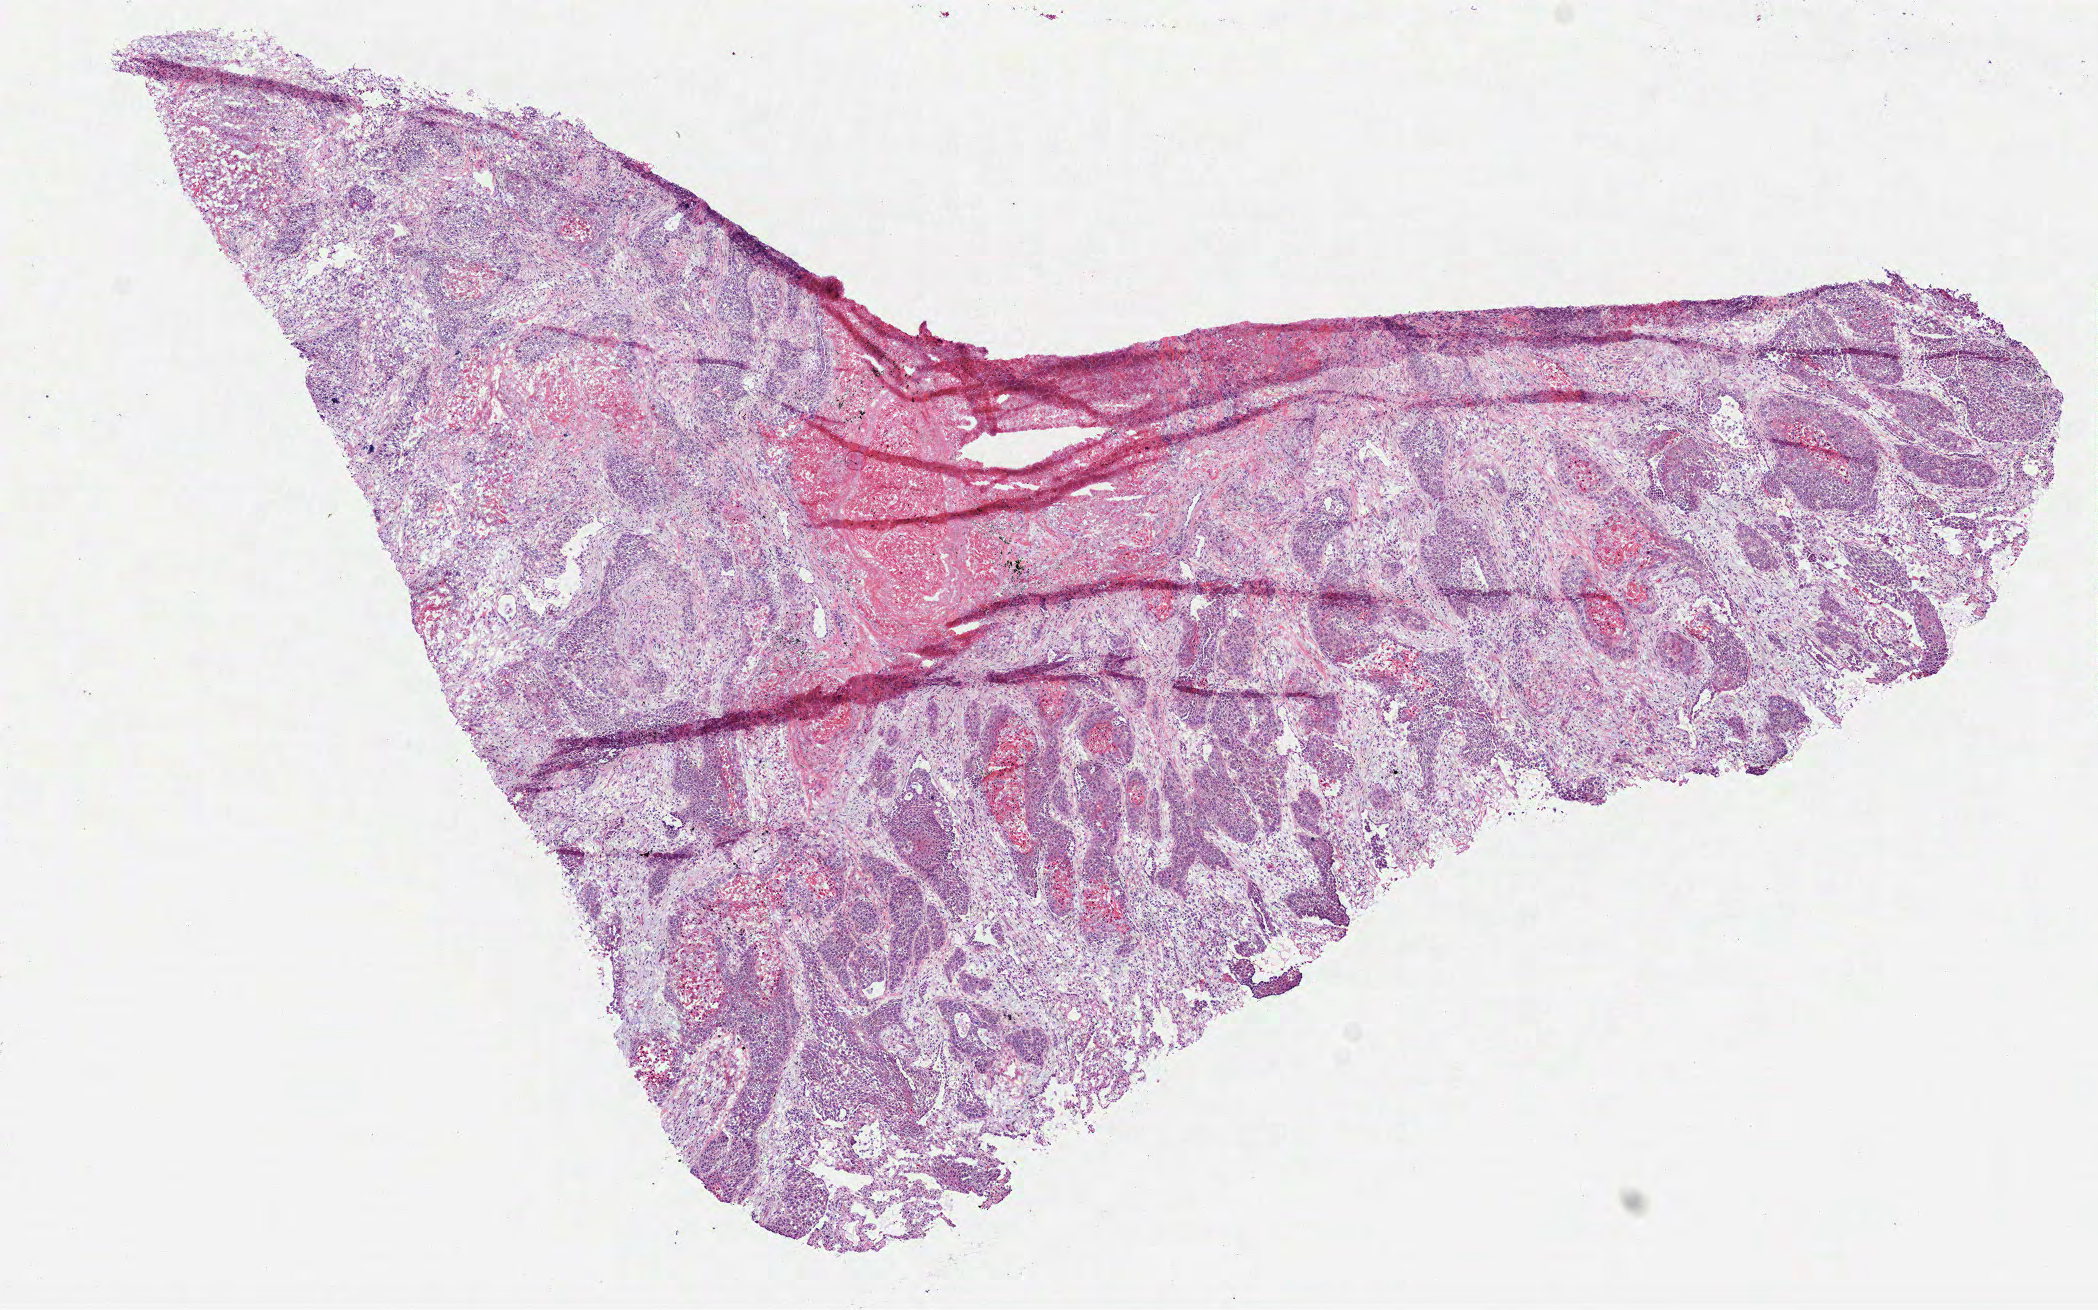
Digitized H&E tissue section (whole slide), low-resolution overview of the scanned area, about 8.5 x 5.3 mm. Frozen section. Primary tumour sample from the lung. Male, age 84 years at initial diagnosis. Pathologist review of this section (percent, as recorded): tumour cells 70%, tumour nuclei 65%, normal cells 0%, stromal cells 15%, necrosis 15%. Inflammatory infiltration, as recorded: lymphocyte infiltration 20%.
Histologic diagnosis: Squamous cell carcinoma, NOS (upper lobe, lung). AJCC pathologic stage: IIIA (7th edition). Laterality: left.